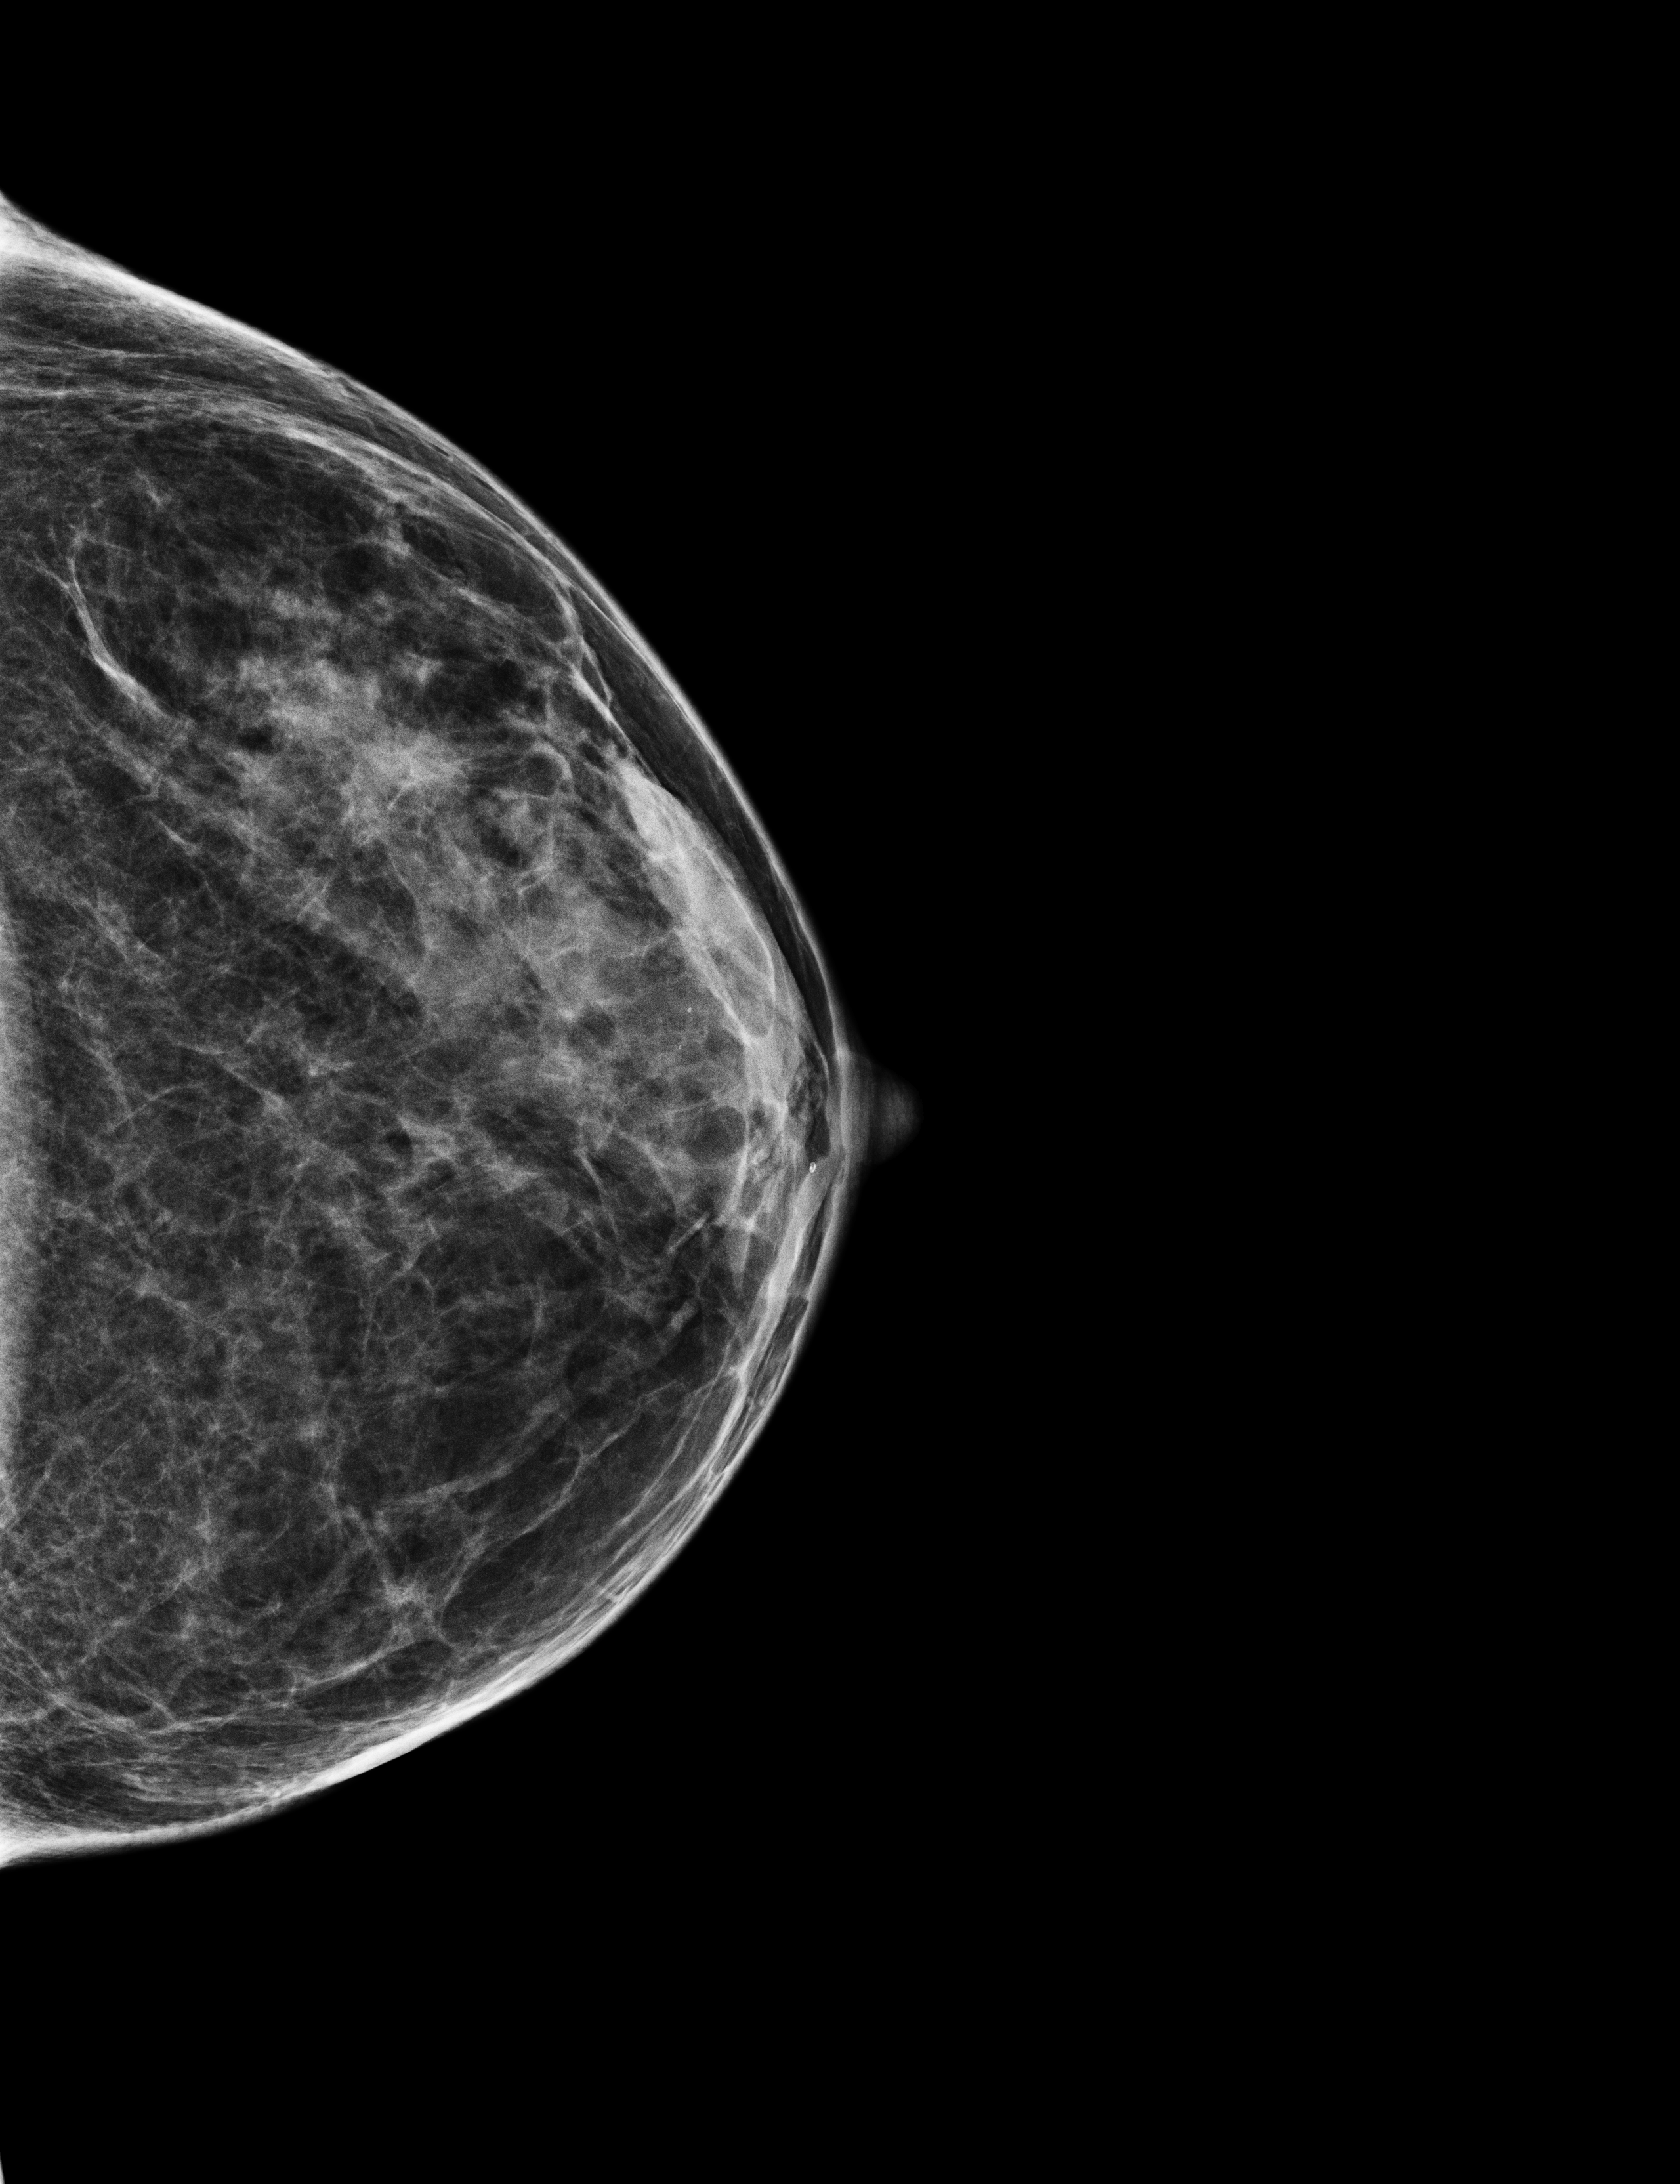
Annual screening mammography examination, compressed breast thickness 43 mm. Female patient, age 47 years.
Image type: full-field digital mammogram. Breast: left. Projection: cranio-caudal projection.